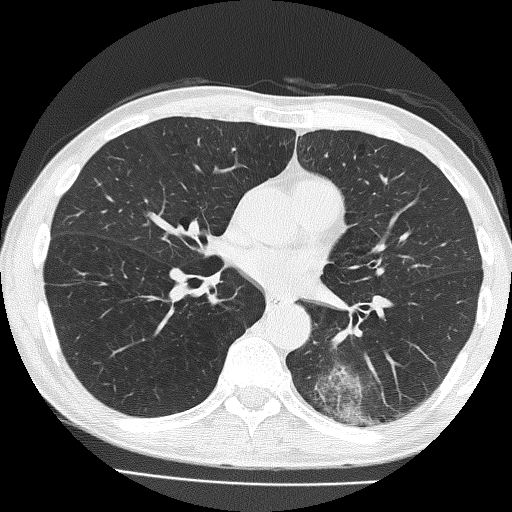
Chest CT (low-dose screening protocol), one axial image. Baseline screening round. Lung window (W 1500 / L -600 HU). 2 mm slice thickness. Lung (sharp) reconstruction kernel (FC51). Slice 82 of 160 in the series. 512 × 512 image matrix. Male participant, aged 58 years at enrolment.
Expert reader's lesion annotation, bounding box [x1, y1, x2, y2] px = [304, 316, 417, 434]. The screening reader recorded 2 non-calcified nodules or masses ≥4 mm on this exam (left lower lobe, left upper lobe); which of them this box marks is not recorded. Lung cancer was diagnosed 39 days after this screen: non-small cell carcinoma, left lower lobe, poorly differentiated (G3), stage IV (AJCC 6th edition), 74 mm at pathology.